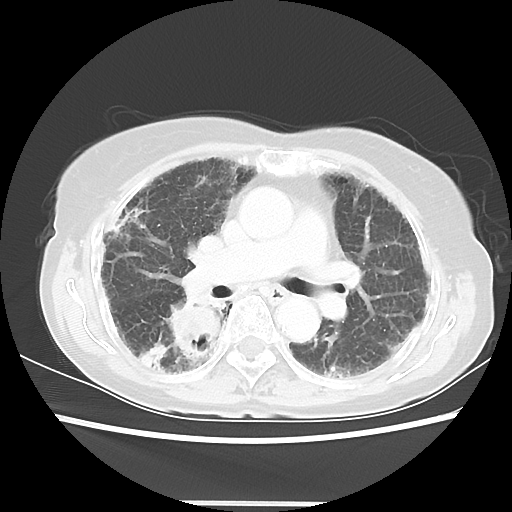
Chest CT, one axial slice. Slice 31 of 52 in the series (ordered by position). Reconstruction kernel LUNG. Lung window (W 1500 / L -600 HU). 512 × 512 image matrix, field of view 325 × 325 mm. Patient: female, 71 years. Case-level facts recorded for this patient, not image findings: clinical TNM (as recorded): T3 N0 M0.
Outlined on this slice (bounding box drawn by a radiologist):
- lung tumour (recorded histology: squamous cell carcinoma): bounding box (x1, y1, x2, y2) in pixels: (165, 294, 219, 361)